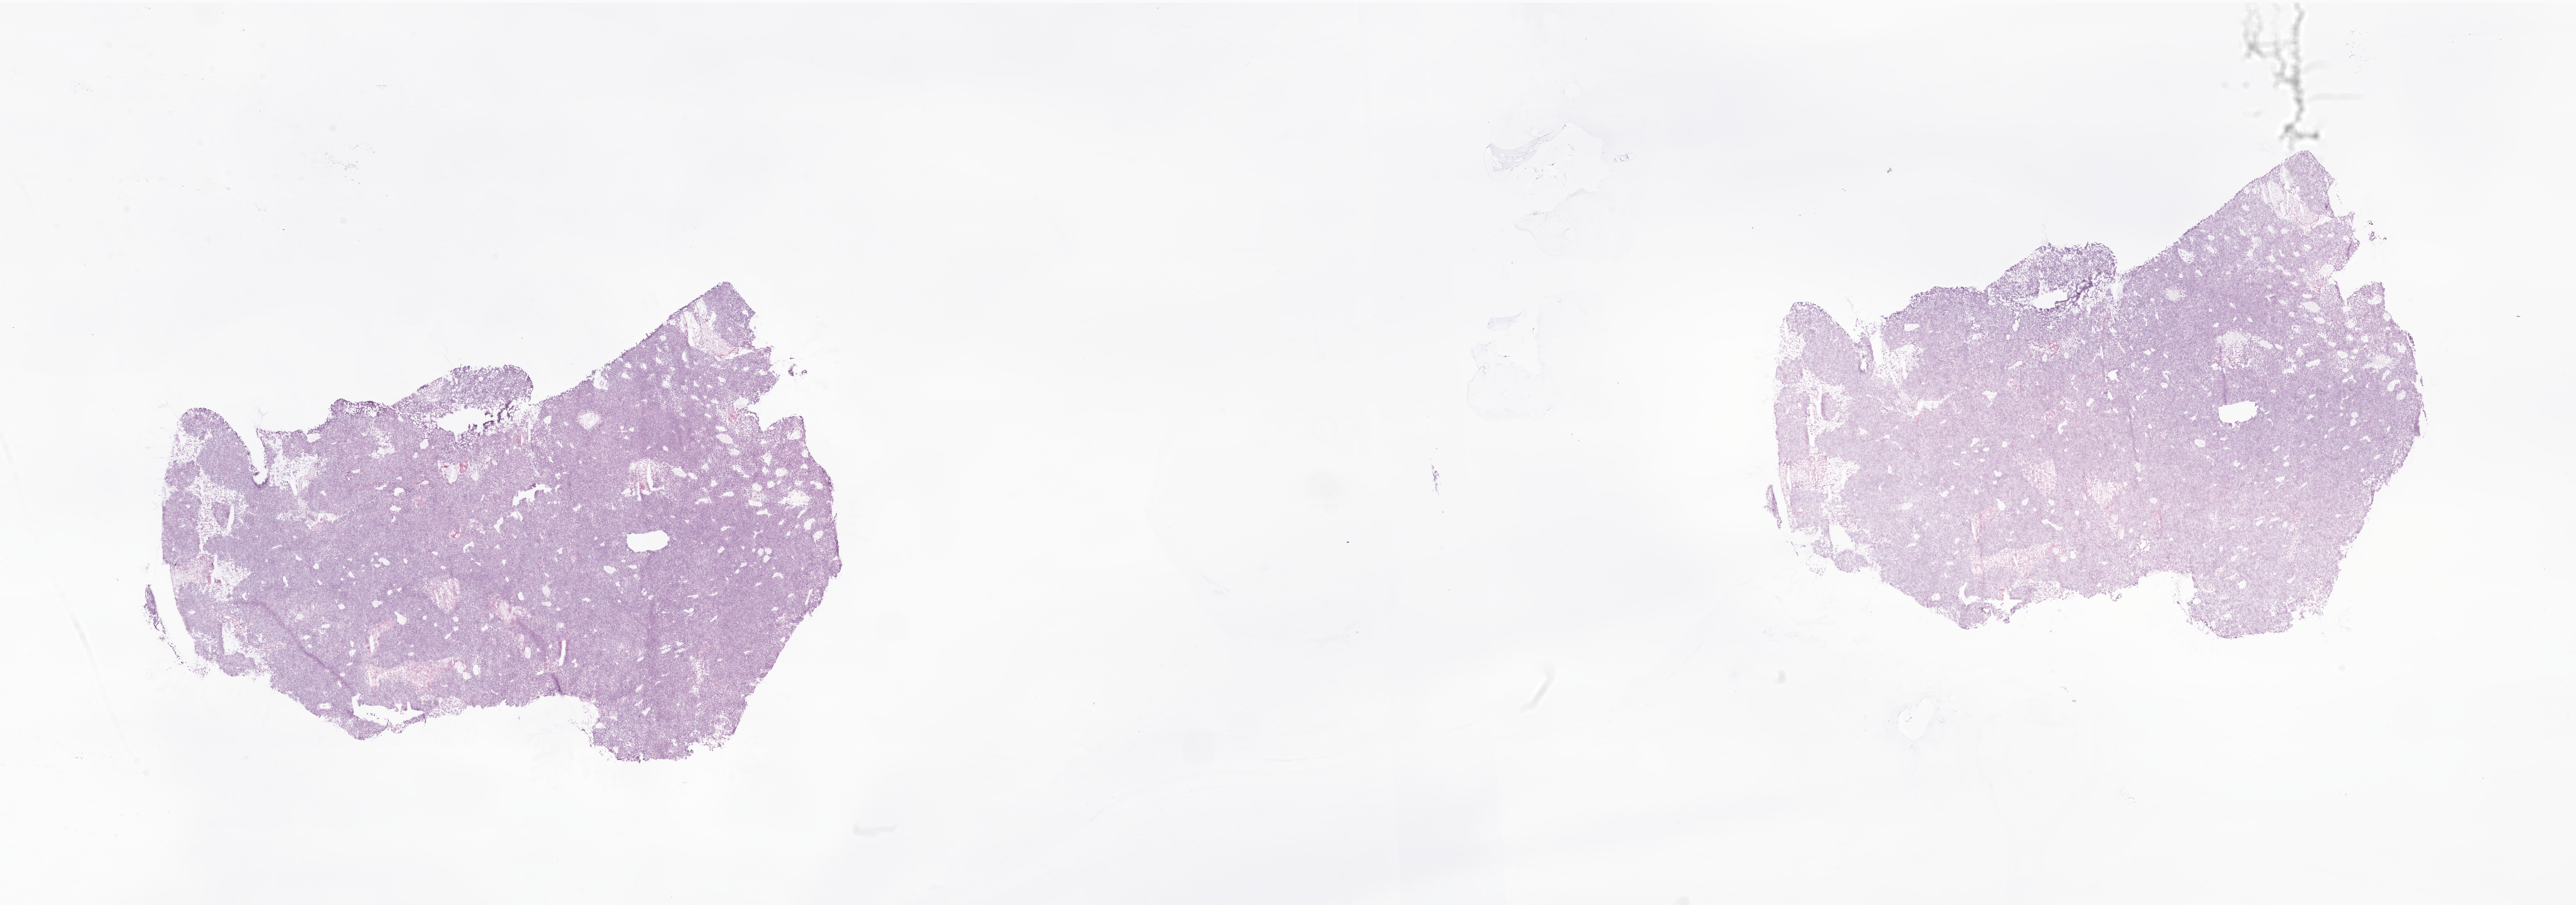
Digitized hematoxylin and eosin (H&E)-stained section of tumor tissue from the brain, shown as a low-resolution overview of the whole scanned area (about 34.1 x 12.0 mm). Frozen section (OCT-embedded). Patient: female, age 51 days.
Recorded diagnosis: Neoplasm, malignant.